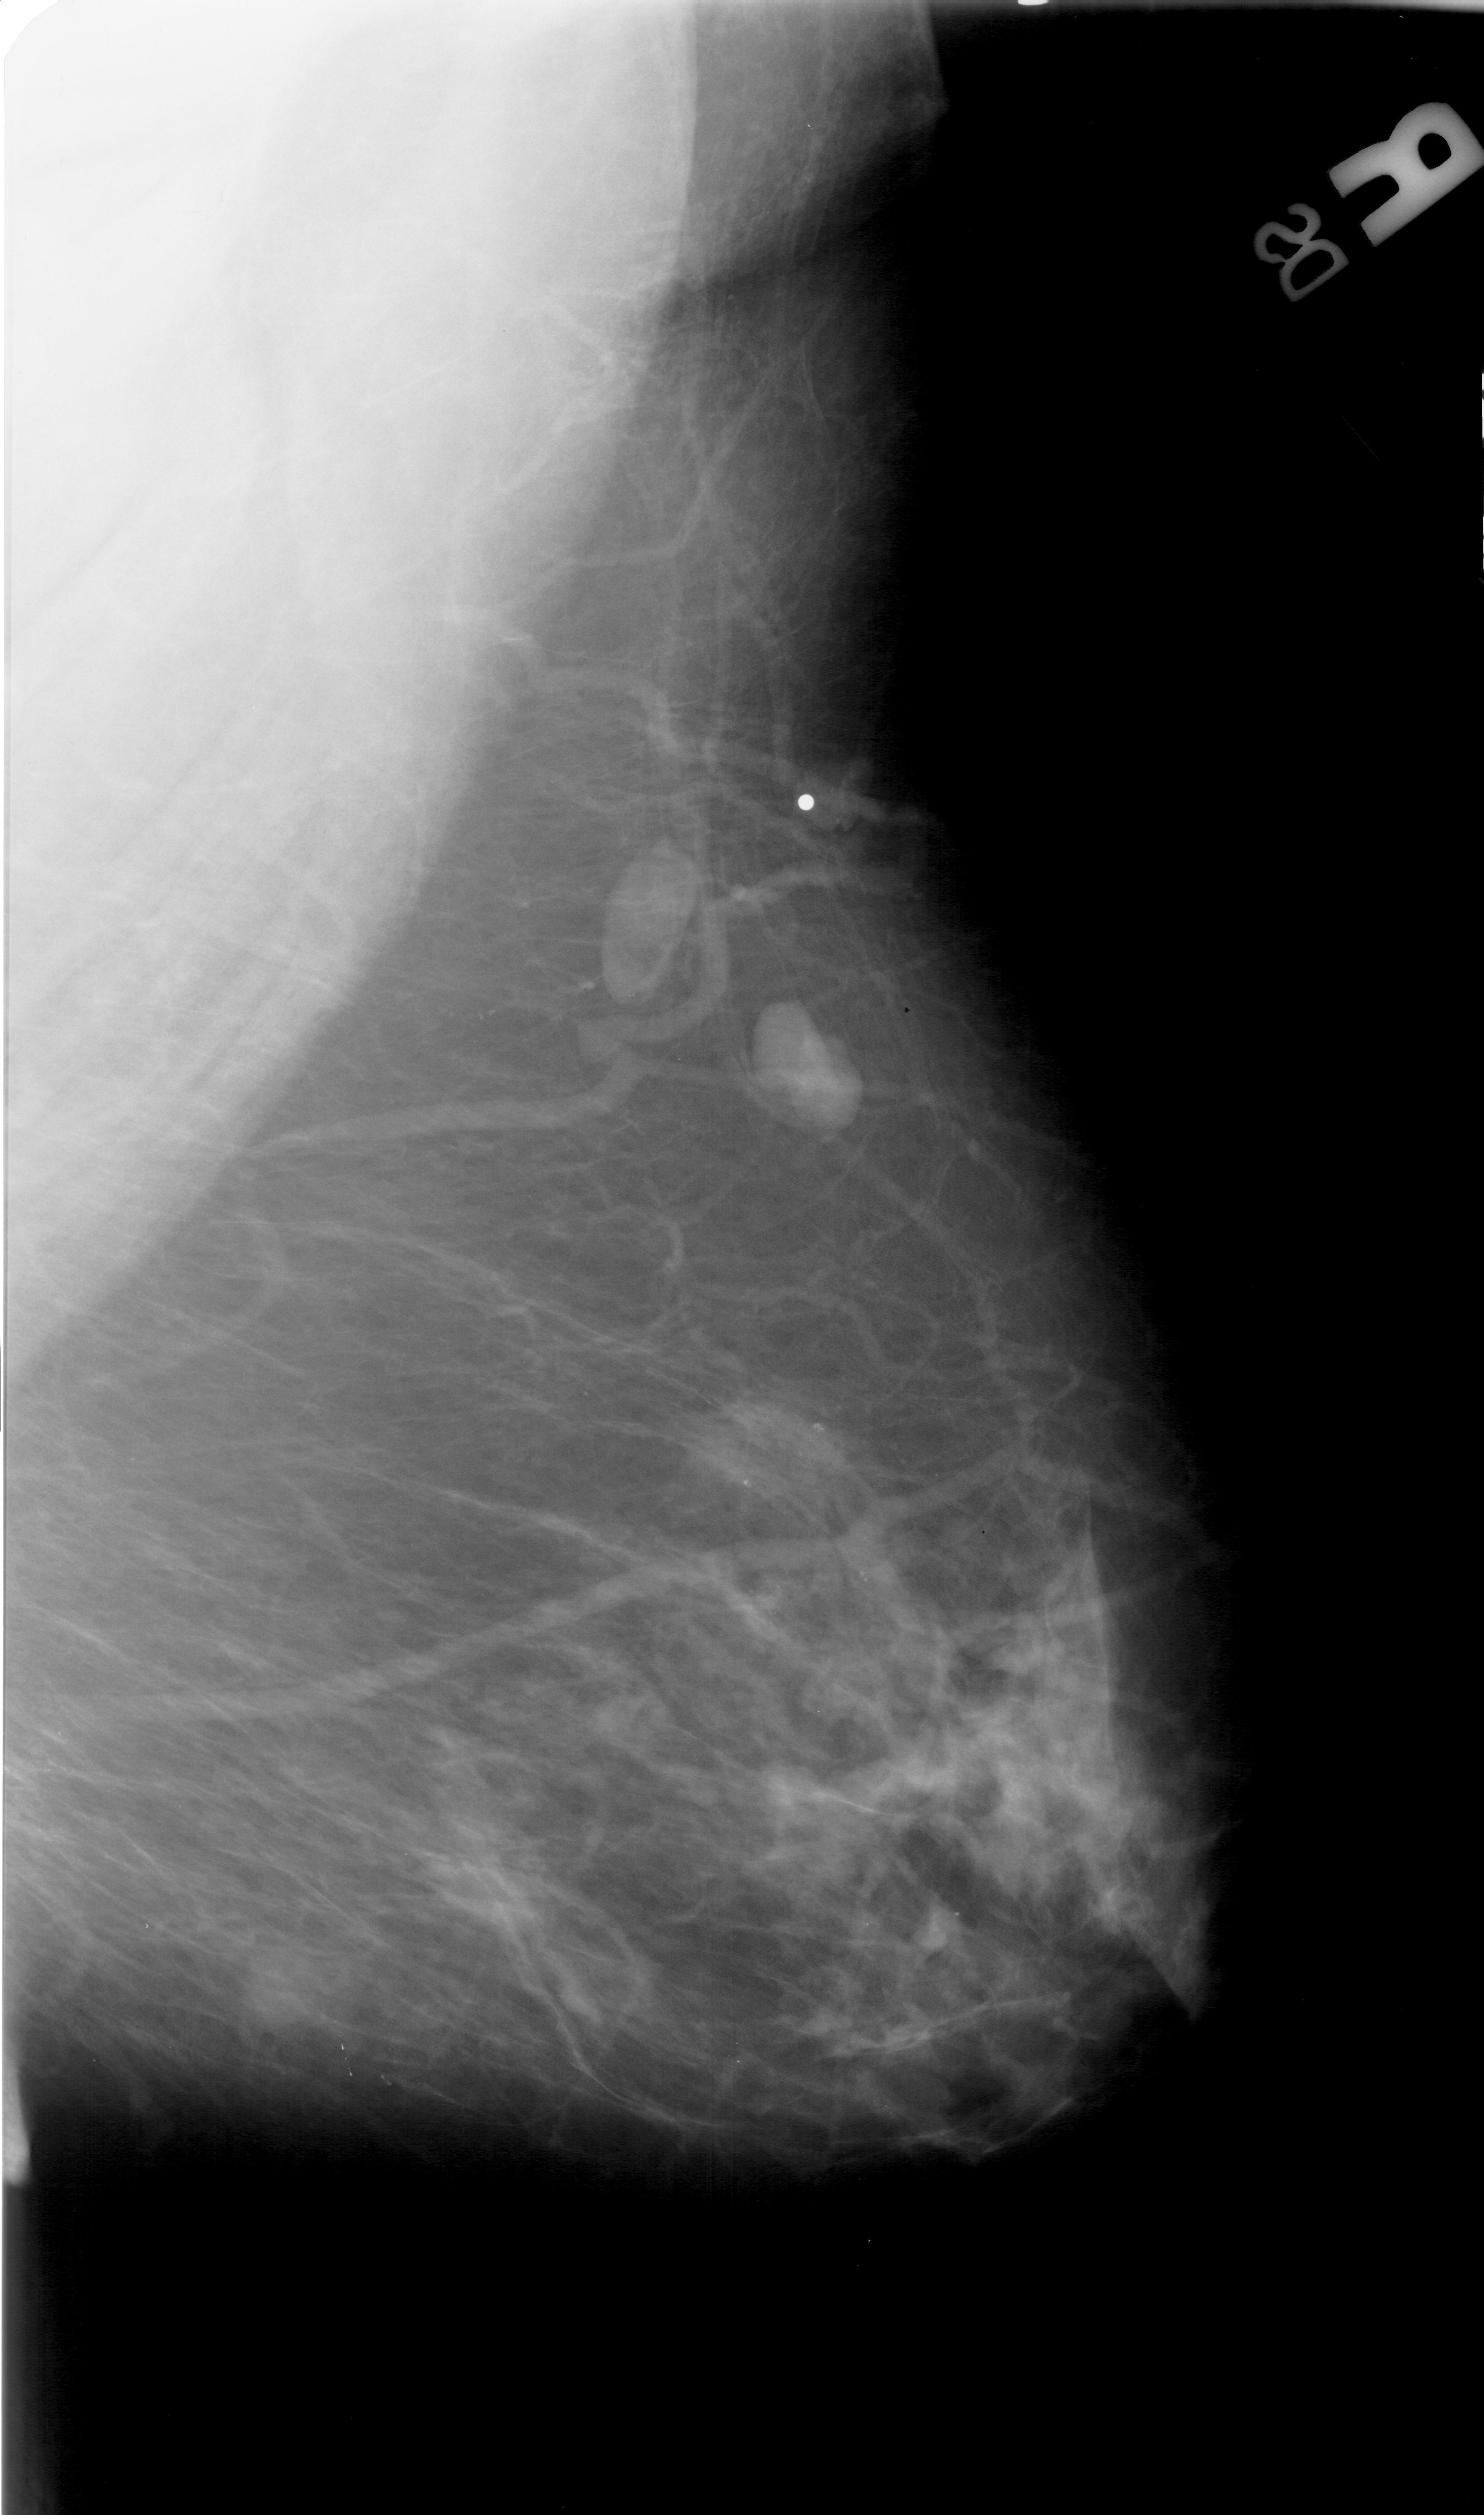
Digitized screen-film mammogram; right breast; MLO view; BI-RADS breast density category 2 (scale 1–4); 1484 × 2515 image matrix.
Expert-marked regions of interest on this image (one box per marked abnormality):
- calcifications, morphology pleomorphic, distribution clustered; BI-RADS assessment category 3; pathology result (as recorded, not read from the image): benign: bounding box [x1, y1, x2, y2] px = [815, 1555, 886, 1617]